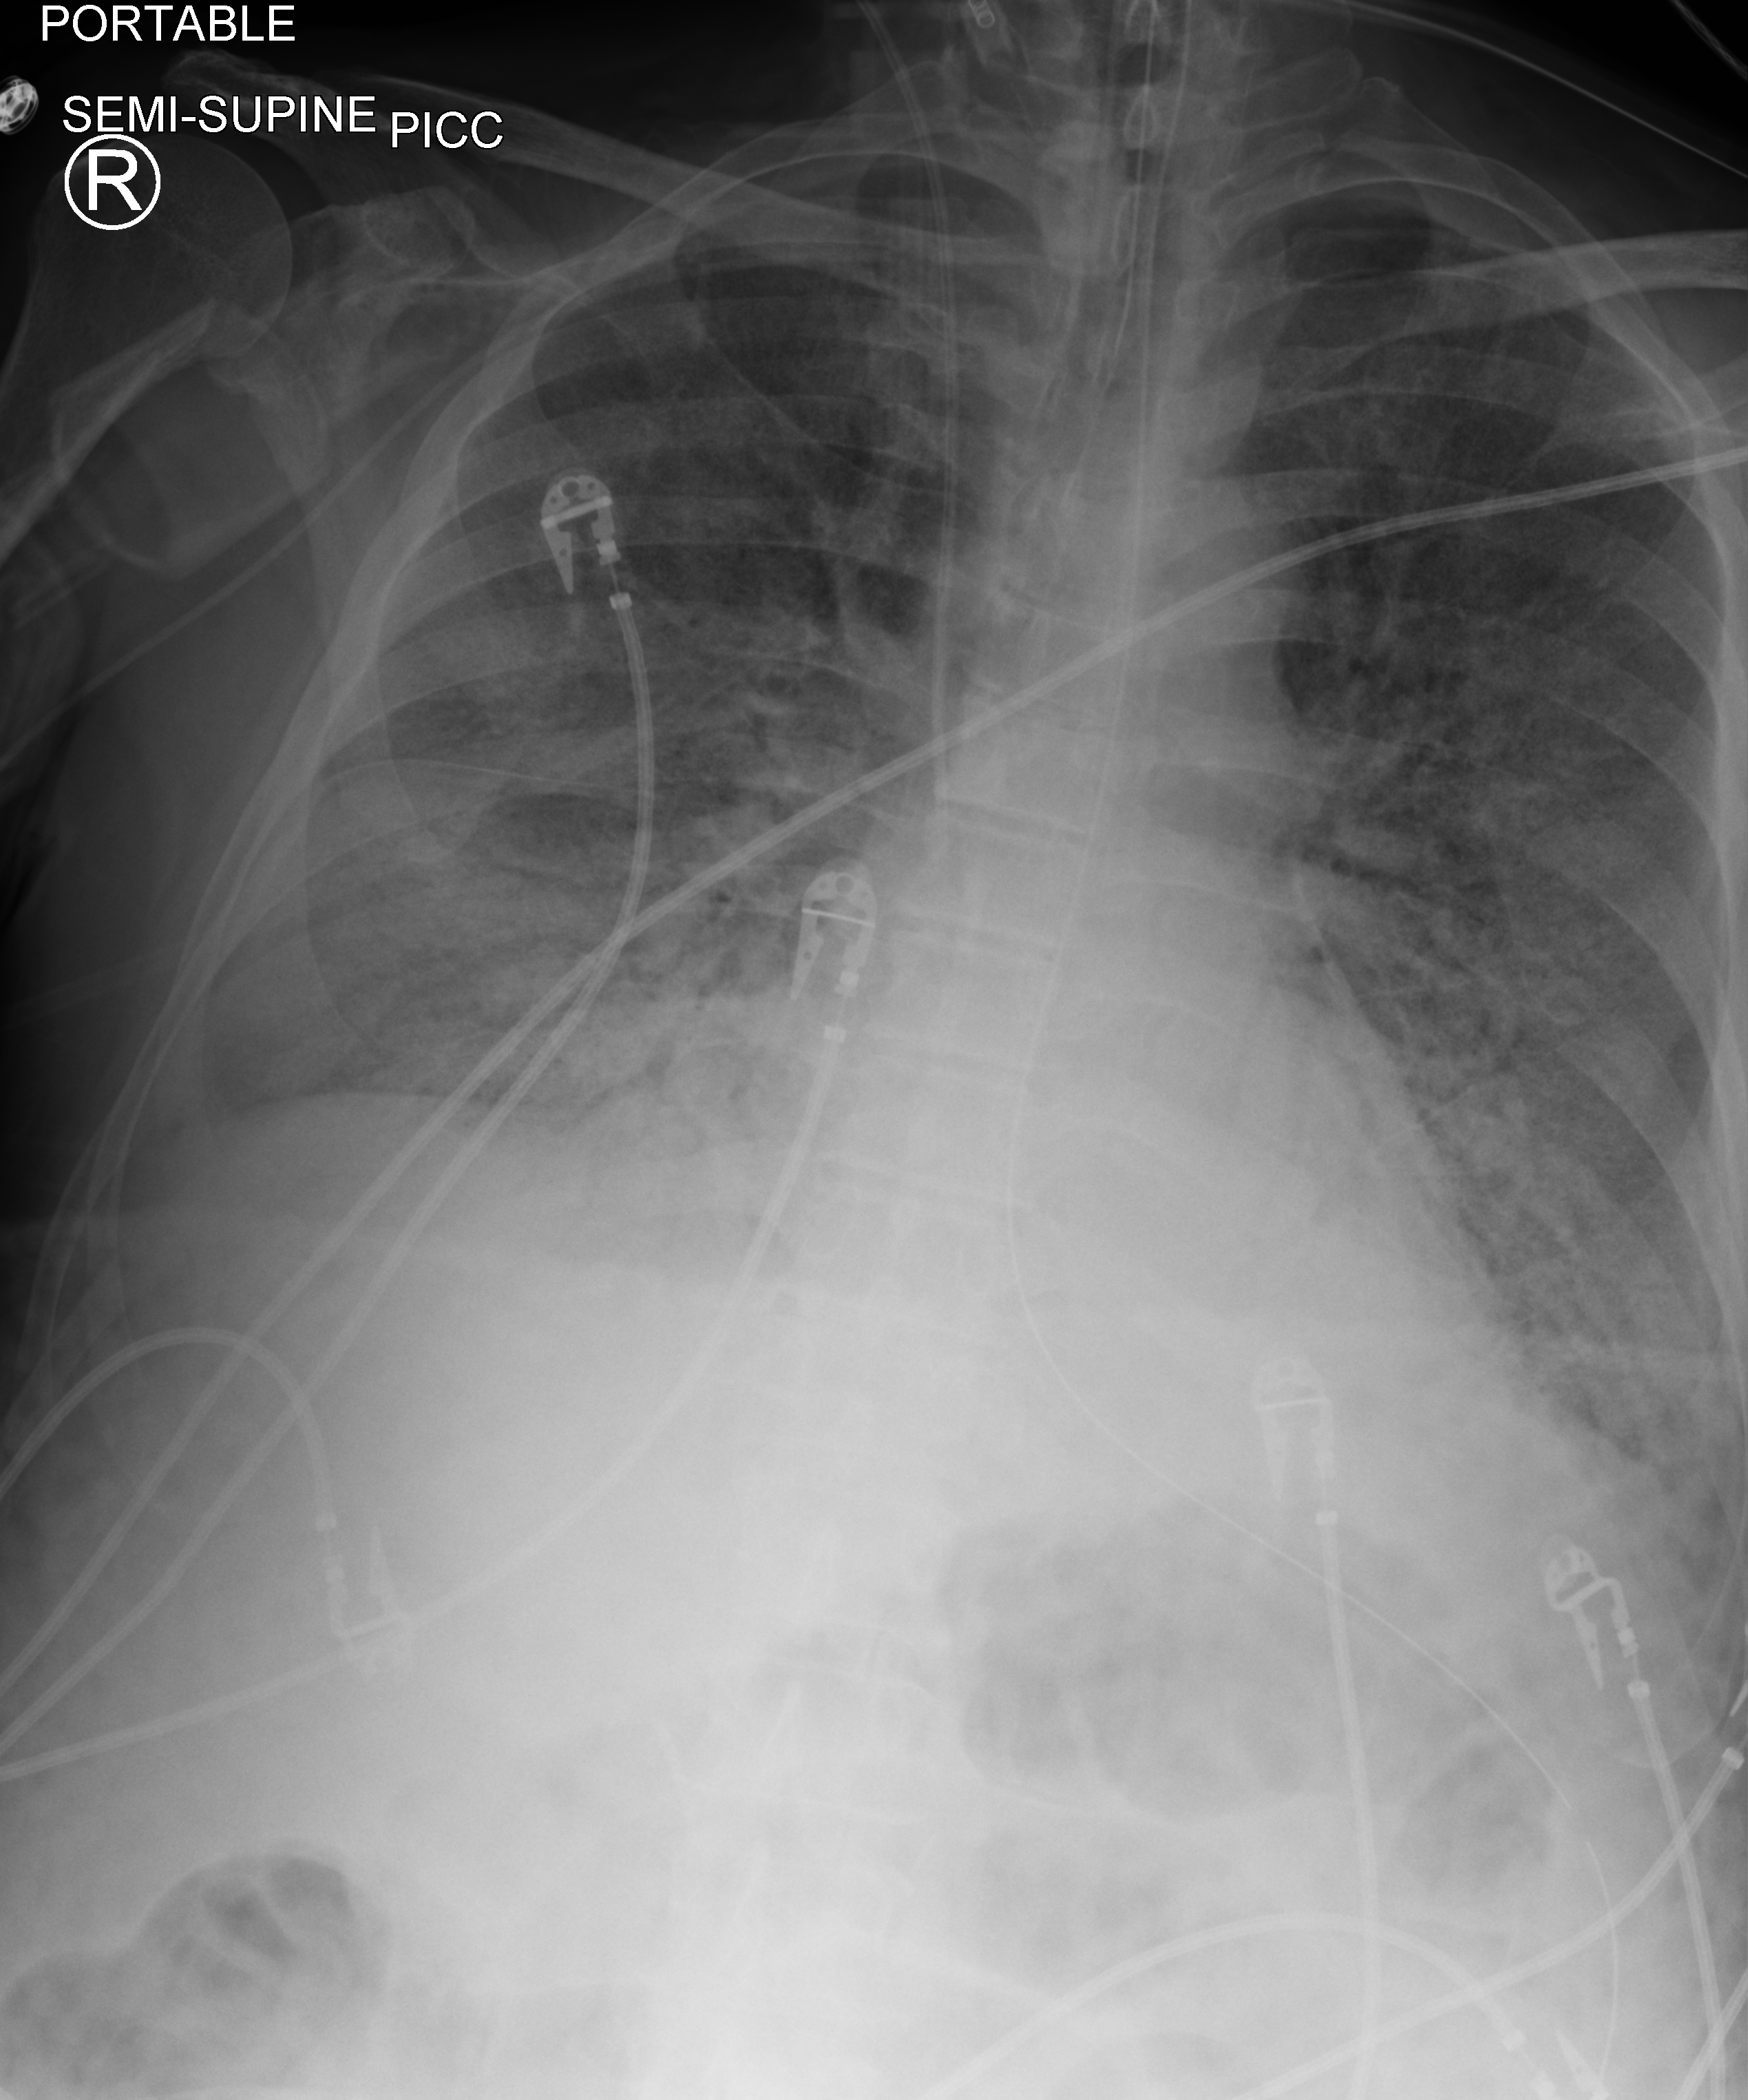
Portable chest radiograph. Male patient hospitalised with COVID-19, age 60–74 years.
Admission-level facts for this patient (not findings on this image; timing relative to this image not recorded):
- chronic kidney disease (admission record): no
- admitted to intensive care during this hospital stay: yes